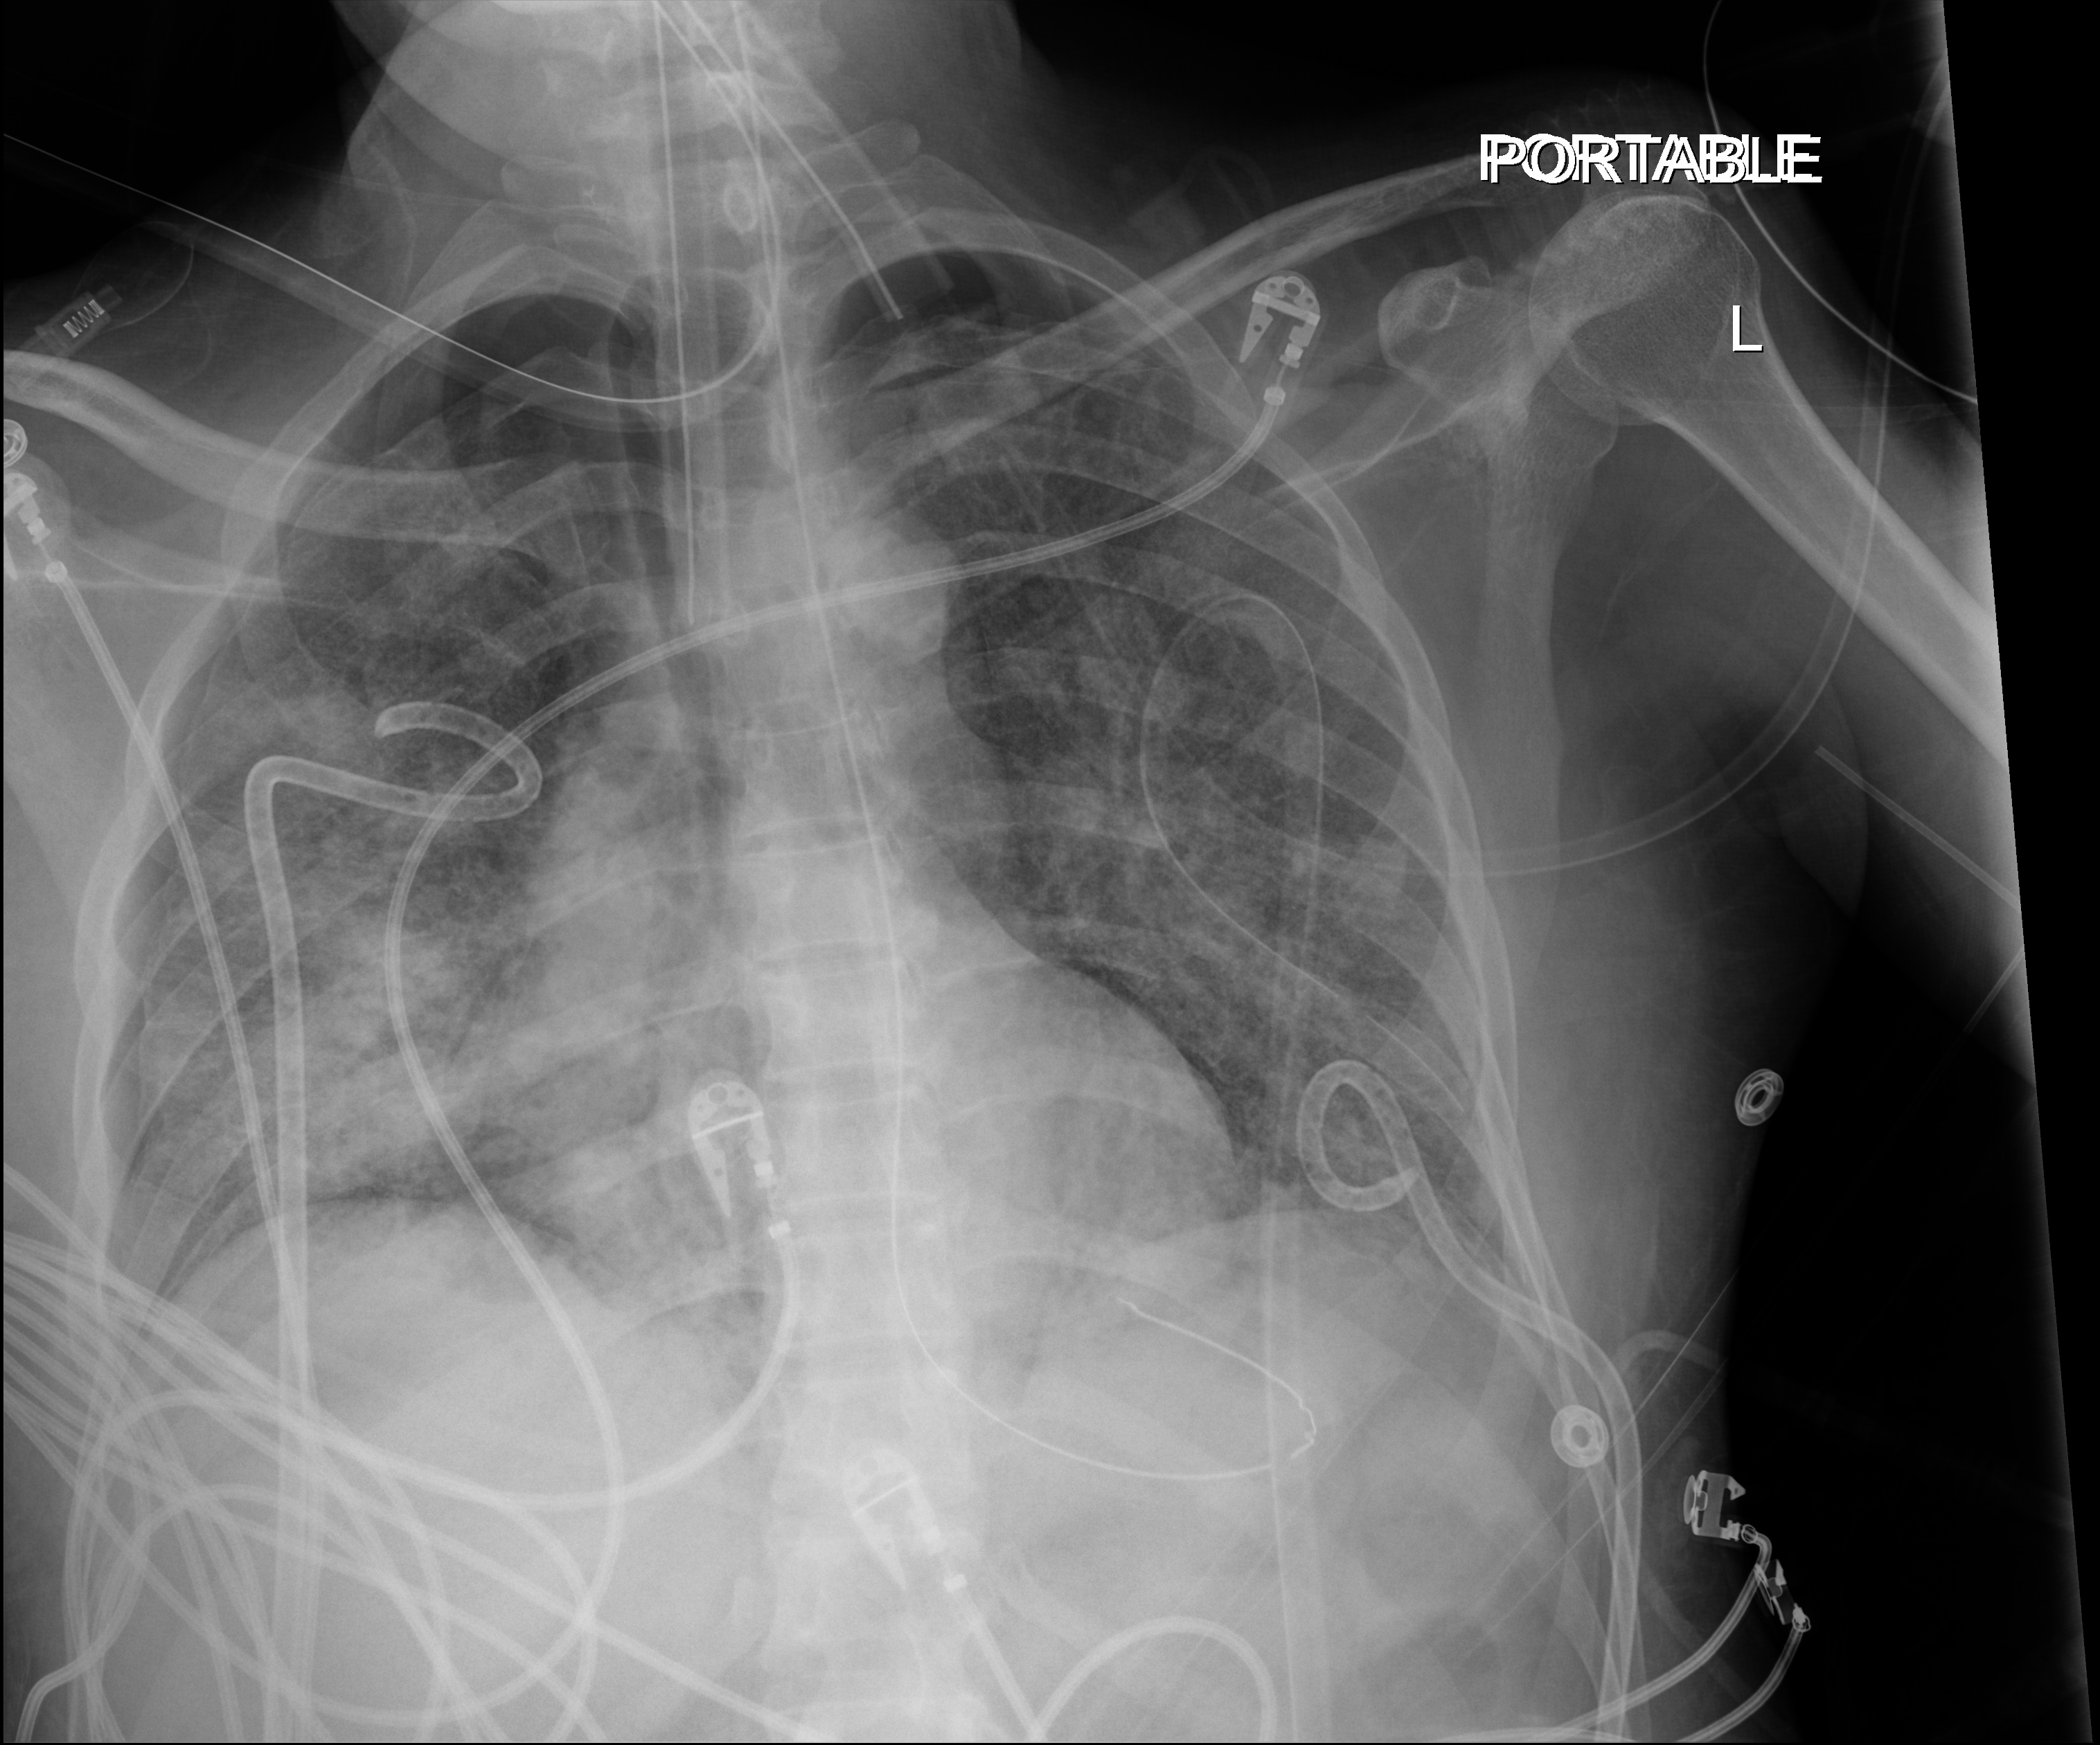
Chest X-ray; anteroposterior (AP) projection. Adult patient hospitalised with COVID-19, age 18–59 years.
Hospital-stay facts (about this admission, not read from this image; timing relative to this image not recorded):
- admitted to intensive care during this hospital stay: yes
- length of hospital stay: 41 days